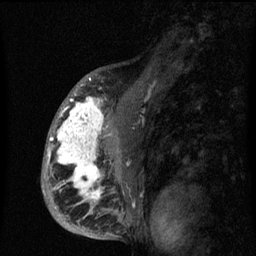
Breast MRI (dynamic contrast-enhanced), one sagittal slice; position 41 of 60 along the scan axis; dynamic contrast-enhanced series, image 2 of 3 at this slice position (ordered by acquisition); 1.5 T; TE 4.2 ms, TR 8 ms; 2 mm slice thickness; 256 × 256 image matrix, field of view 190 × 190 mm. Patient: female, 50 years.
Annotated regions visible in this slice (semi-automatic segmentation, software-assisted and operator-edited):
- analysis volume of interest (the breast-tissue region the enhancement analysis was run in; not a lesion): bounding box [x1, y1, x2, y2] px = [43, 90, 142, 216]
- tumour enhancement mask (voxels above the 70 % enhancement threshold inside the analysis volume of interest): [47, 91, 117, 213]